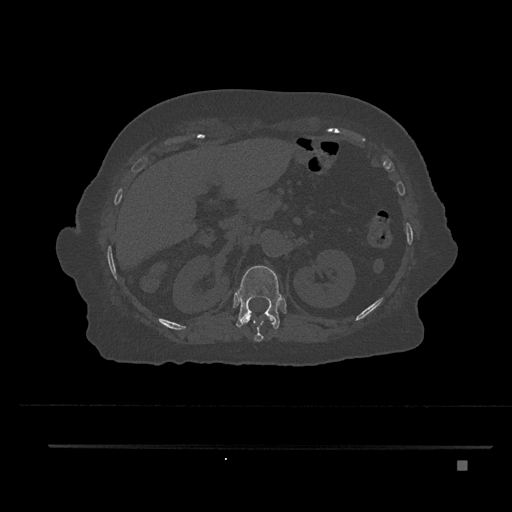
CT including the spine, one axial slice. Reconstruction kernel Br40s/3. 120 kVp. Bone window (W 1800 / L 400 HU). 0.5 mm slice thickness. 512 × 512 image matrix. Patient: female, 76 years. From the clinical record (not read from this slice): primary cancer: lung; vertebrae with lytic lesions (as recorded): T11, L3.
Outlined on this slice (semi-automatically segmented with operator editing):
- T11 vertebra: bounding box <242,313,275,342> (left, top, right, bottom; pixels)
- T12 vertebra: <236,265,282,330>